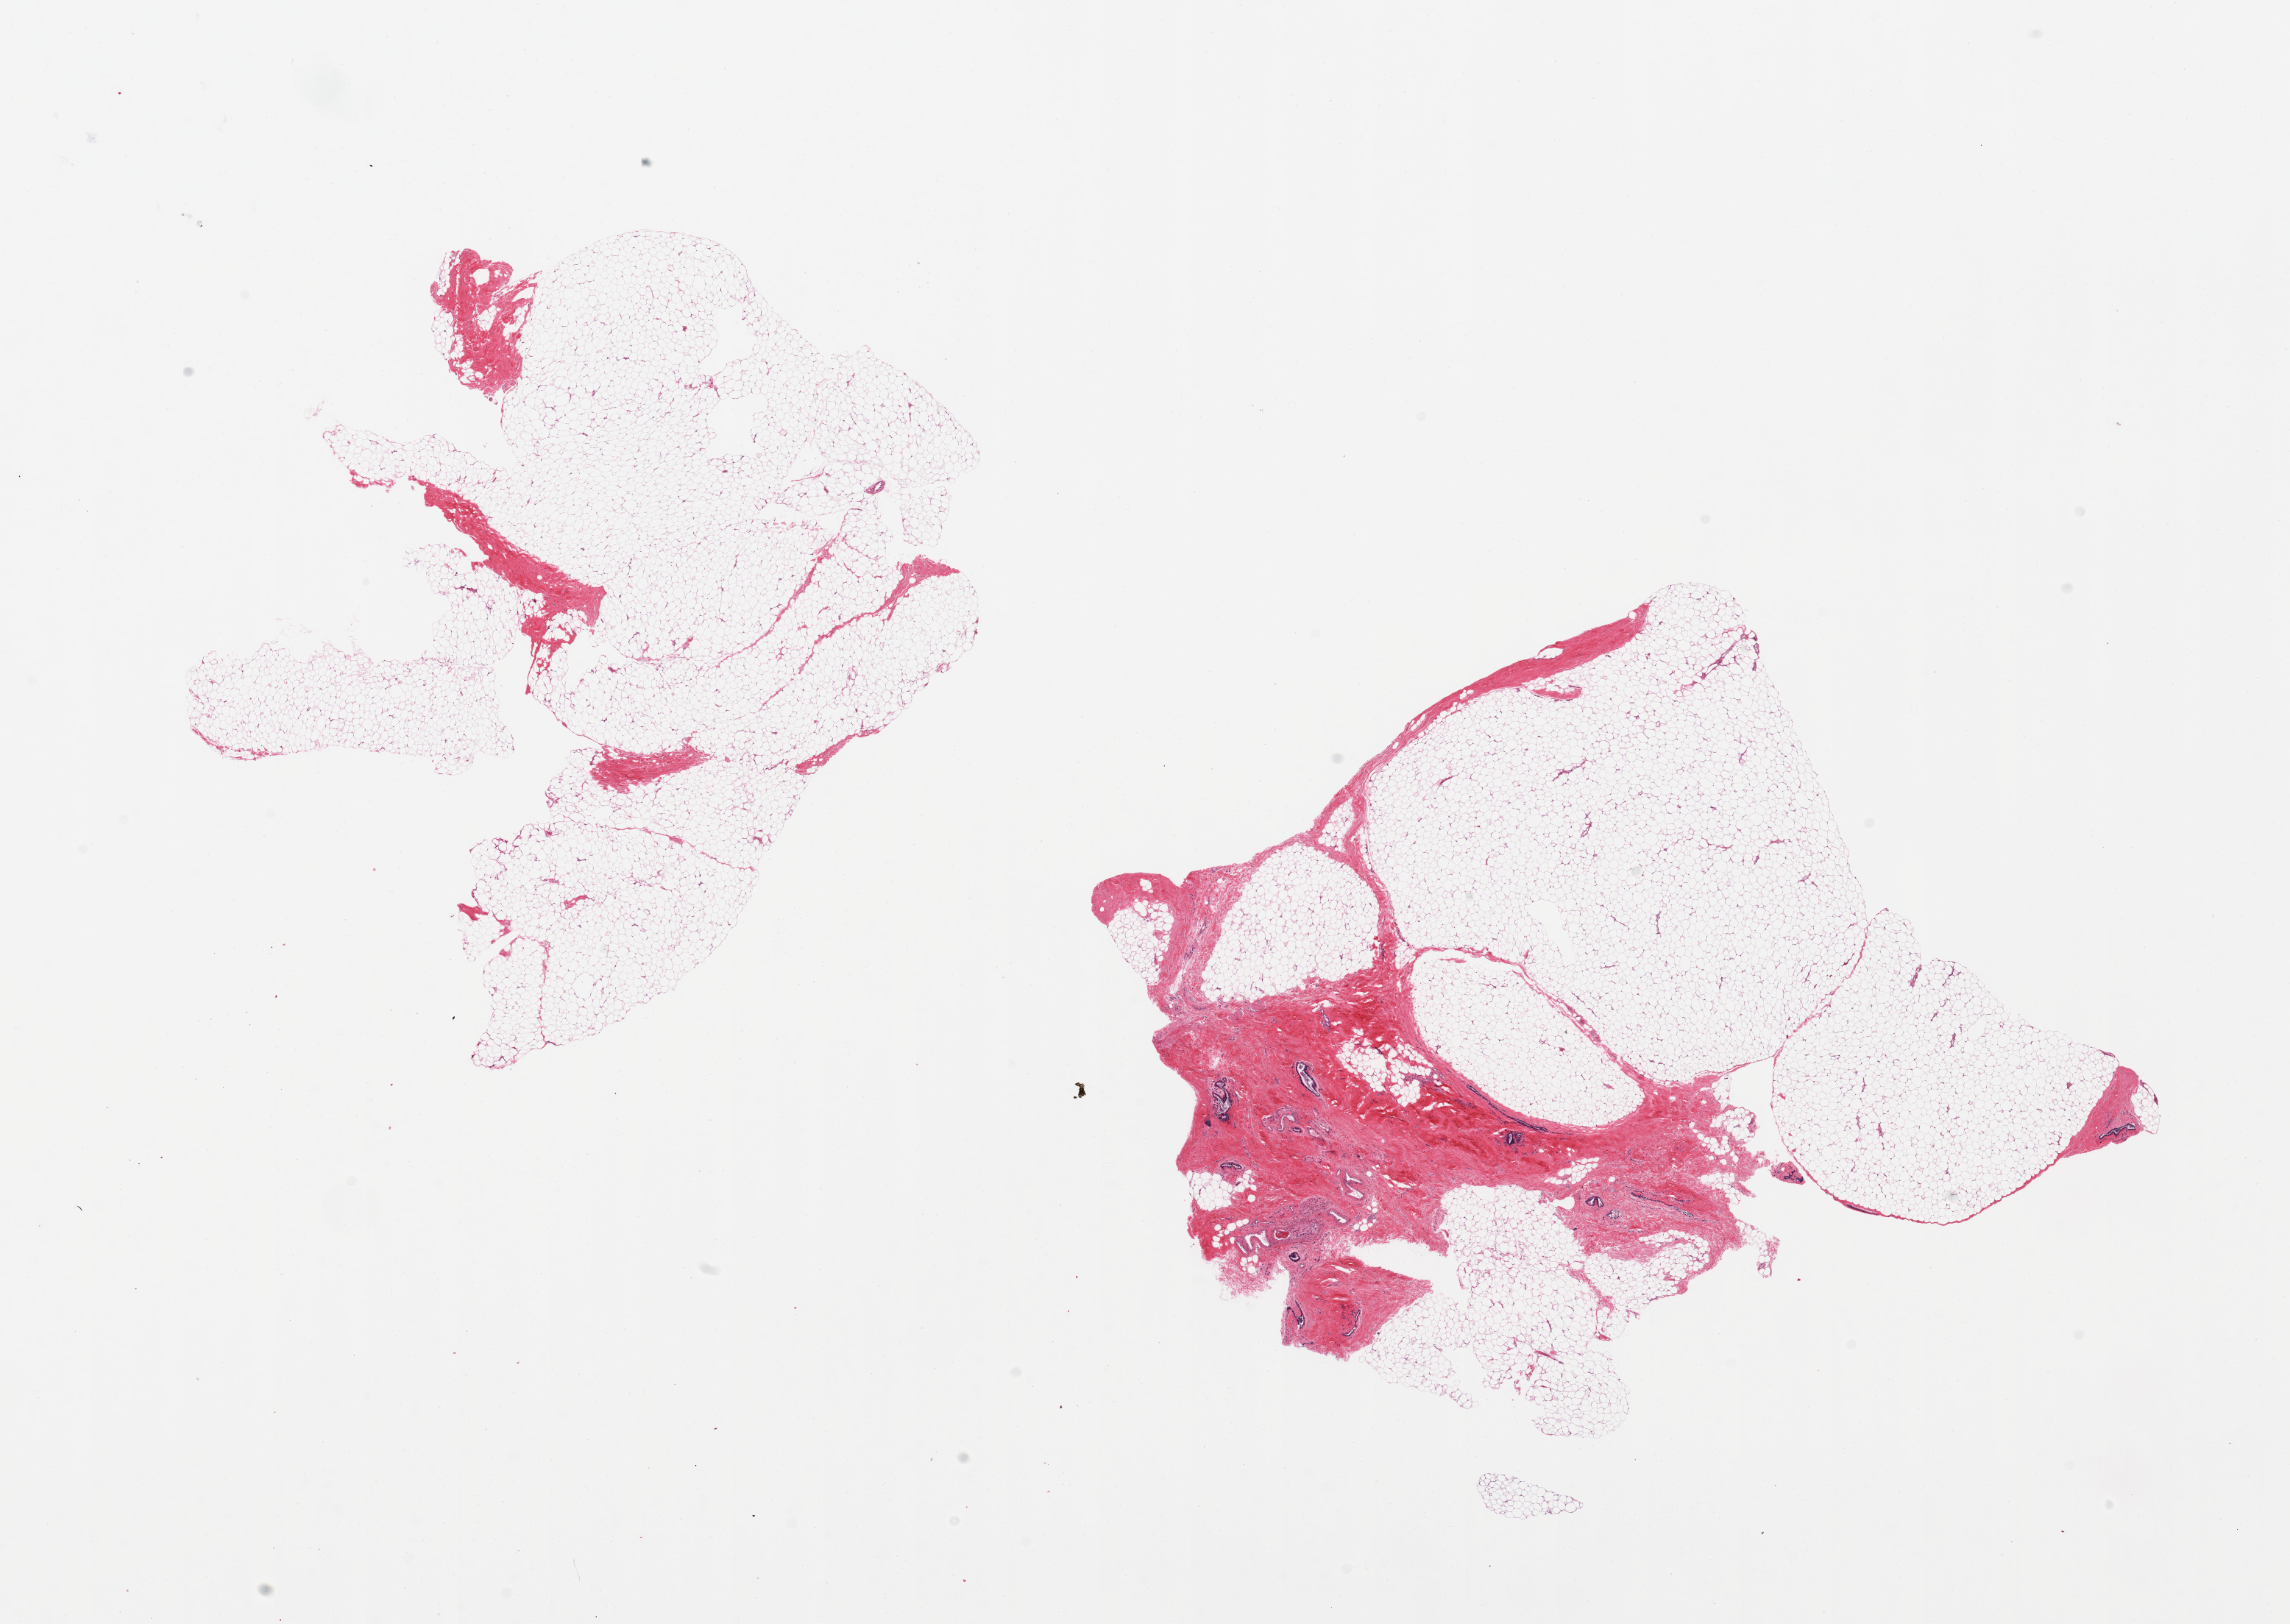
Digitized hematoxylin and eosin (H&E)-stained section, a low-resolution overview of the entire scanned area, about 24.6 x 17.5 mm (slide scanned at 20x), PAXgene-fixed paraffin-embedded (PFPE) section, sampled site (target tissue): breast, donor tissue sample. Male donor.
Pathologist's review note for this sample: 2 pieces; fibroadipose with ducts in one; over 90% adipose in other.